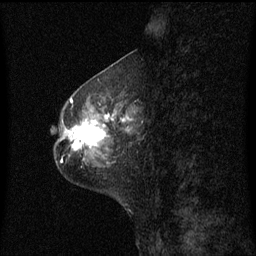
Breast MRI (dynamic contrast-enhanced), one sagittal slice. Position 23 of 60 along the scan axis. Dynamic contrast-enhanced series, image 2 of 3 at this slice position (ordered by acquisition). 1.5 T. TE 4.2 ms, TR 8.4 ms. 256 × 256 image matrix, field of view 200 × 200 mm. Female patient, age 49 years. Case-level facts recorded for this patient, not image findings: setting: breast cancer imaged before/during neoadjuvant chemotherapy; receptor status: HR-positive, HER2-negative.
Outlined on this slice (semi-automatically segmented with operator editing):
- analysis volume of interest (the breast-tissue region the enhancement analysis was run in; not a lesion): bounding box (x1, y1, x2, y2) in pixels: (59, 101, 138, 158)
- tumour enhancement mask (voxels above the 70 % enhancement threshold inside the analysis volume of interest): (69, 112, 130, 151)